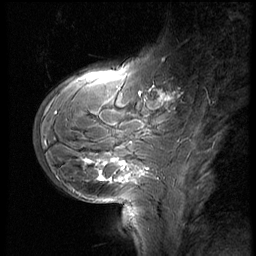
Breast MRI (dynamic contrast-enhanced), one sagittal slice; position 18 of 60 along the scan axis; 3 images stored at this slice position (order not interpretable as contrast timing); 1.5 T; TE 4.2 ms, TR 8.9 ms; 256 × 256 image matrix, field of view 200 × 200 mm. Female patient, age 29 years. Case-level facts recorded for this patient, not image findings: setting: breast cancer imaged before/during neoadjuvant chemotherapy.
Outlined on this slice (semi-automatic segmentation, software-assisted and operator-edited):
- analysis volume of interest (the breast-tissue region the enhancement analysis was run in; not a lesion): bounding box <35,57,185,200> (left, top, right, bottom; pixels)
- tumour enhancement mask (voxels above the 140 % enhancement threshold inside the analysis volume of interest): <86,86,170,184>